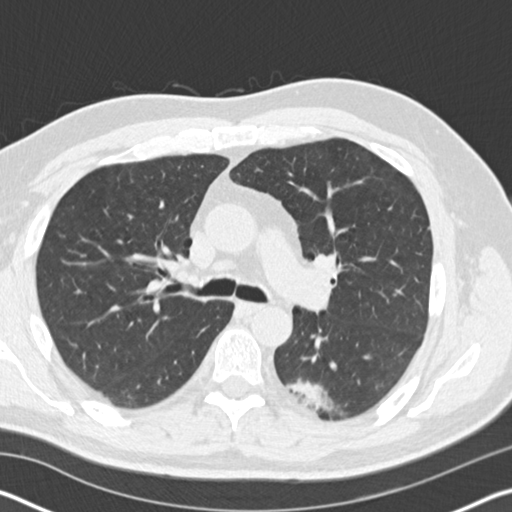
Axial slice from a low-dose chest CT screening exam. Baseline screening round. Lung window (W 1500 / L -600 HU). 2 mm slice thickness. Standard (soft-tissue) reconstruction kernel (B30f). 120 kVp. Slice 69 of 178 in the series. Male, age 60 years at enrolment.
• Lesion marked by an expert reader, box from (x=277, y=365) to (x=358, y=425) px.
• The screening reader recorded 3 non-calcified nodules or masses ≥4 mm on this exam (left lower lobe, right lower lobe, right lower lobe); which of them this box marks is not recorded.
• Official screen result: positive, change unspecified: nodule(s) >= 4 mm or enlarging nodule(s), mass(es), or other non-specific abnormalities suspicious for lung cancer.